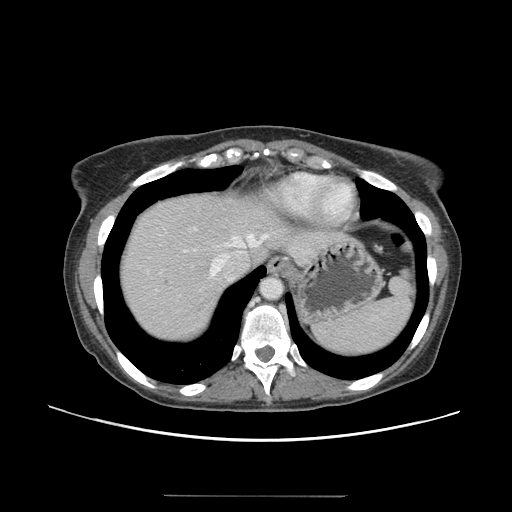
Contrast-enhanced abdominal CT, one axial slice; position 124 of 144 along the scan axis; intravenous contrast given; soft-tissue window (W 400 / L 40 HU); 2.5 mm slice thickness; 512 × 512 image matrix. Female patient, age 53 years. From the clinical record (not read from this slice): diagnosis: colorectal cancer liver metastases, imaged before liver resection.
Structures marked on this image (manually delineated by an expert):
- hepatic veins: bounding box [x1, y1, x2, y2] px = [211, 234, 268, 276]
- liver: [120, 194, 310, 341]
- planned liver remnant (the part of the liver to remain after resection): [120, 192, 269, 296]